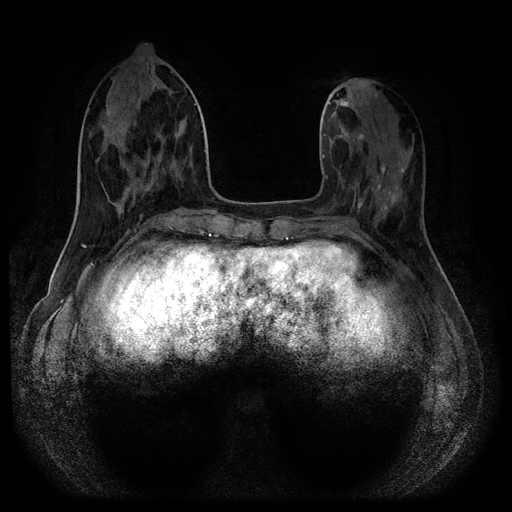
Breast MRI (dynamic contrast-enhanced, multi-phase), one axial slice. Slice 40 of 116 in the series (ordered by position). Dynamic contrast-enhanced series, time point 2 of 5 at this slice position (early post-contrast). 1.5 T. TE 2.7 ms, TR 5.4 ms. 2 mm slice thickness. 512 × 512 image matrix, field of view 340 × 340 mm. Patient: female, 40 years.
Outlined on this slice (semi-automatic segmentation, software-assisted and operator-edited):
- breast lesion (labelled benign in the annotation): box from (x=337, y=99) to (x=350, y=107) px